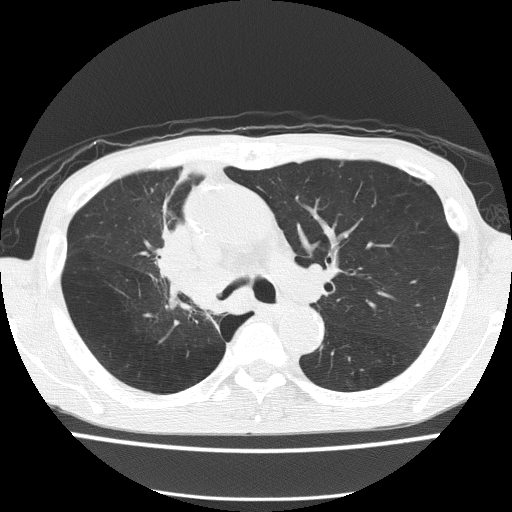
Low-dose screening chest CT, one axial slice. Slice 98 of 150 in the series (ordered by position). Reconstruction kernel FC51. Lung window (W 1500 / L -600 HU). 2 mm slice thickness. 512 × 512 image matrix.
Outlined on this slice (expert manual segmentation):
- lesion 1 (tumor, hilum of right lung): box from (x=161, y=227) to (x=219, y=309) px